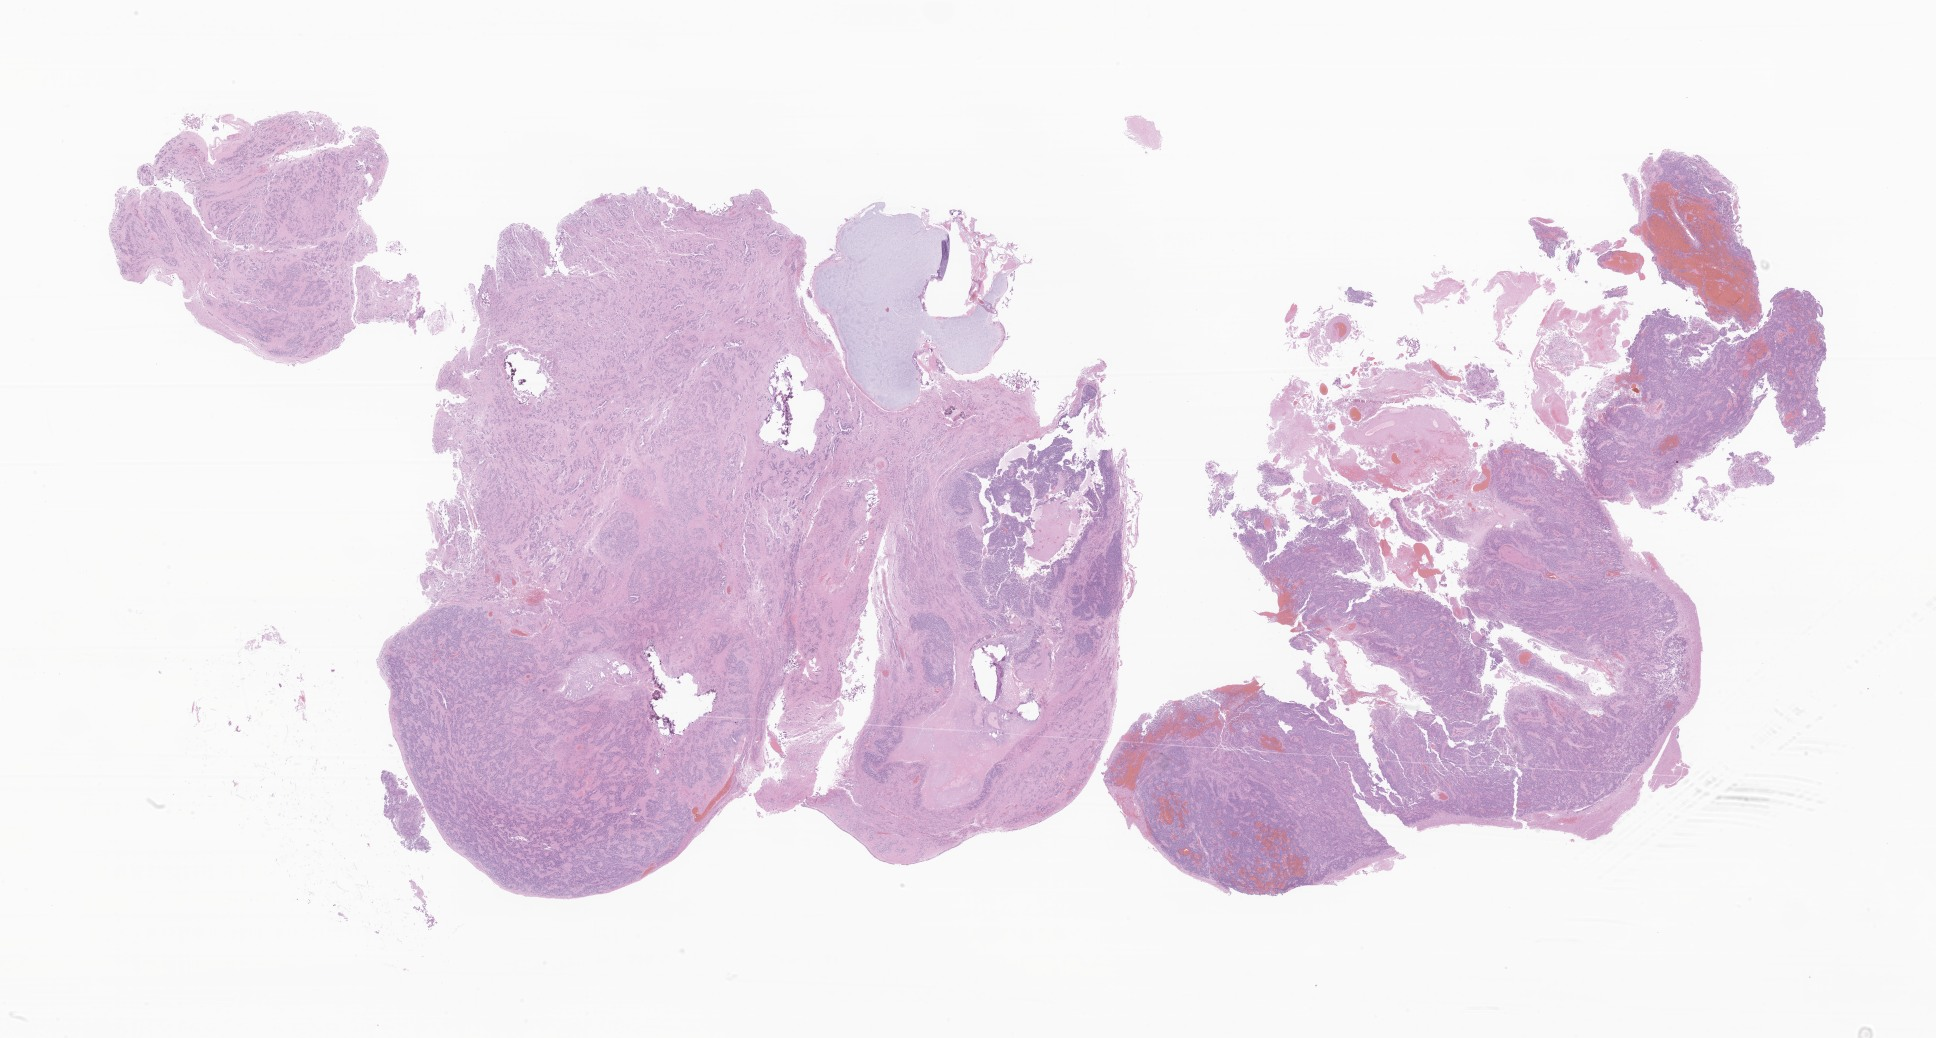
Hematoxylin and eosin (H&E) whole-slide image of tumor tissue from the brain — low-resolution overview of the scanned area, about 32.6 x 17.5 mm; formalin-fixed, paraffin-embedded (FFPE) tissue. Patient: male, age 64 months.
Recorded diagnosis: Ependymoma, NOS.